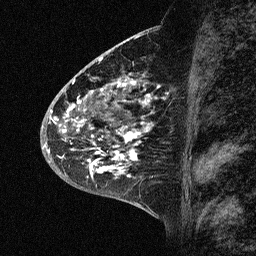
Breast MRI (dynamic contrast-enhanced), one sagittal slice. Slice 26 of 64 in the series (ordered by position). Dynamic contrast-enhanced study with each time point stored as its own series, time point 2 of 3 at this slice position (early post-contrast, ordered by acquisition time). 1.5 T. TE 4.5 ms, TR 11 ms. 2.06 mm slice thickness. 256 × 256 image matrix. Patient: female, 46 years. Case-level facts recorded for this patient, not image findings: setting: breast cancer imaged before/during neoadjuvant chemotherapy; receptor status: HER2-positive.
Structures marked on this image (semi-automatically segmented with operator editing):
- analysis volume of interest (the breast-tissue region the enhancement analysis was run in; not a lesion): bounding box (x1, y1, x2, y2) in pixels: (43, 72, 176, 177)
- tumour enhancement mask (voxels above the 90 % enhancement threshold inside the analysis volume of interest): (55, 73, 149, 177)